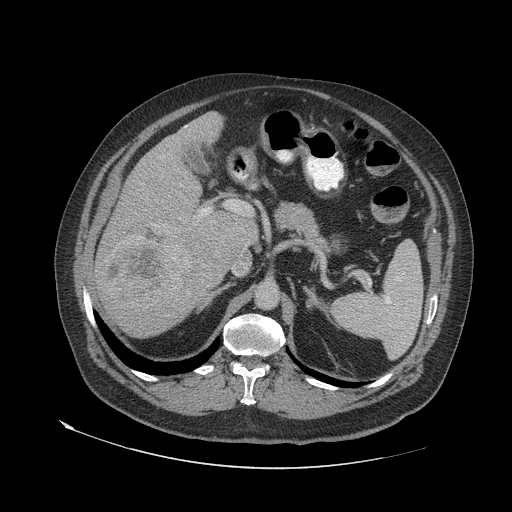
Contrast-enhanced abdominal CT (liver protocol), one axial slice; position 36 of 79 along the scan axis; soft-tissue window (W 400 / L 40 HU); 2.5 mm slice thickness; 512 × 512 image matrix, field of view 480 × 480 mm. From the clinical record (not read from this slice): diagnosis: hepatocellular carcinoma (patient treated with transarterial chemoembolisation; whether this scan precedes or follows treatment is not stated here); TNM stage (as recorded): Stage-IVA; Child-Pugh class: A; tumour differentiation: well differentiated.
Structures marked on this image (semi-automatic segmentation, software-assisted and operator-edited):
- liver parenchyma outside the tumour (the mass and vessels are separate outlines, so this box may not span the whole liver): bounding box <94,112,258,336> (left, top, right, bottom; pixels)
- mass: <96,223,193,311>
- liver vessels: <185,126,248,216>